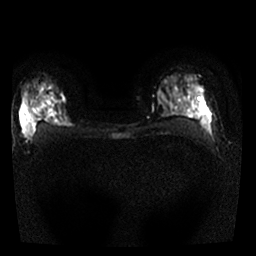
Breast MRI, one axial slice; slice 18 of 25 in the series (ordered by position); diffusion-weighted series; image 2 of 4 stored at this slice position (different b-values; order by instance number); 1.5 T; 4 mm slice thickness; 256 × 256 image matrix. Female patient.
Outlined on this slice (expert manual segmentation):
- tumour on diffusion-weighted imaging: bounding box (x1, y1, x2, y2) in pixels: (21, 98, 66, 138)